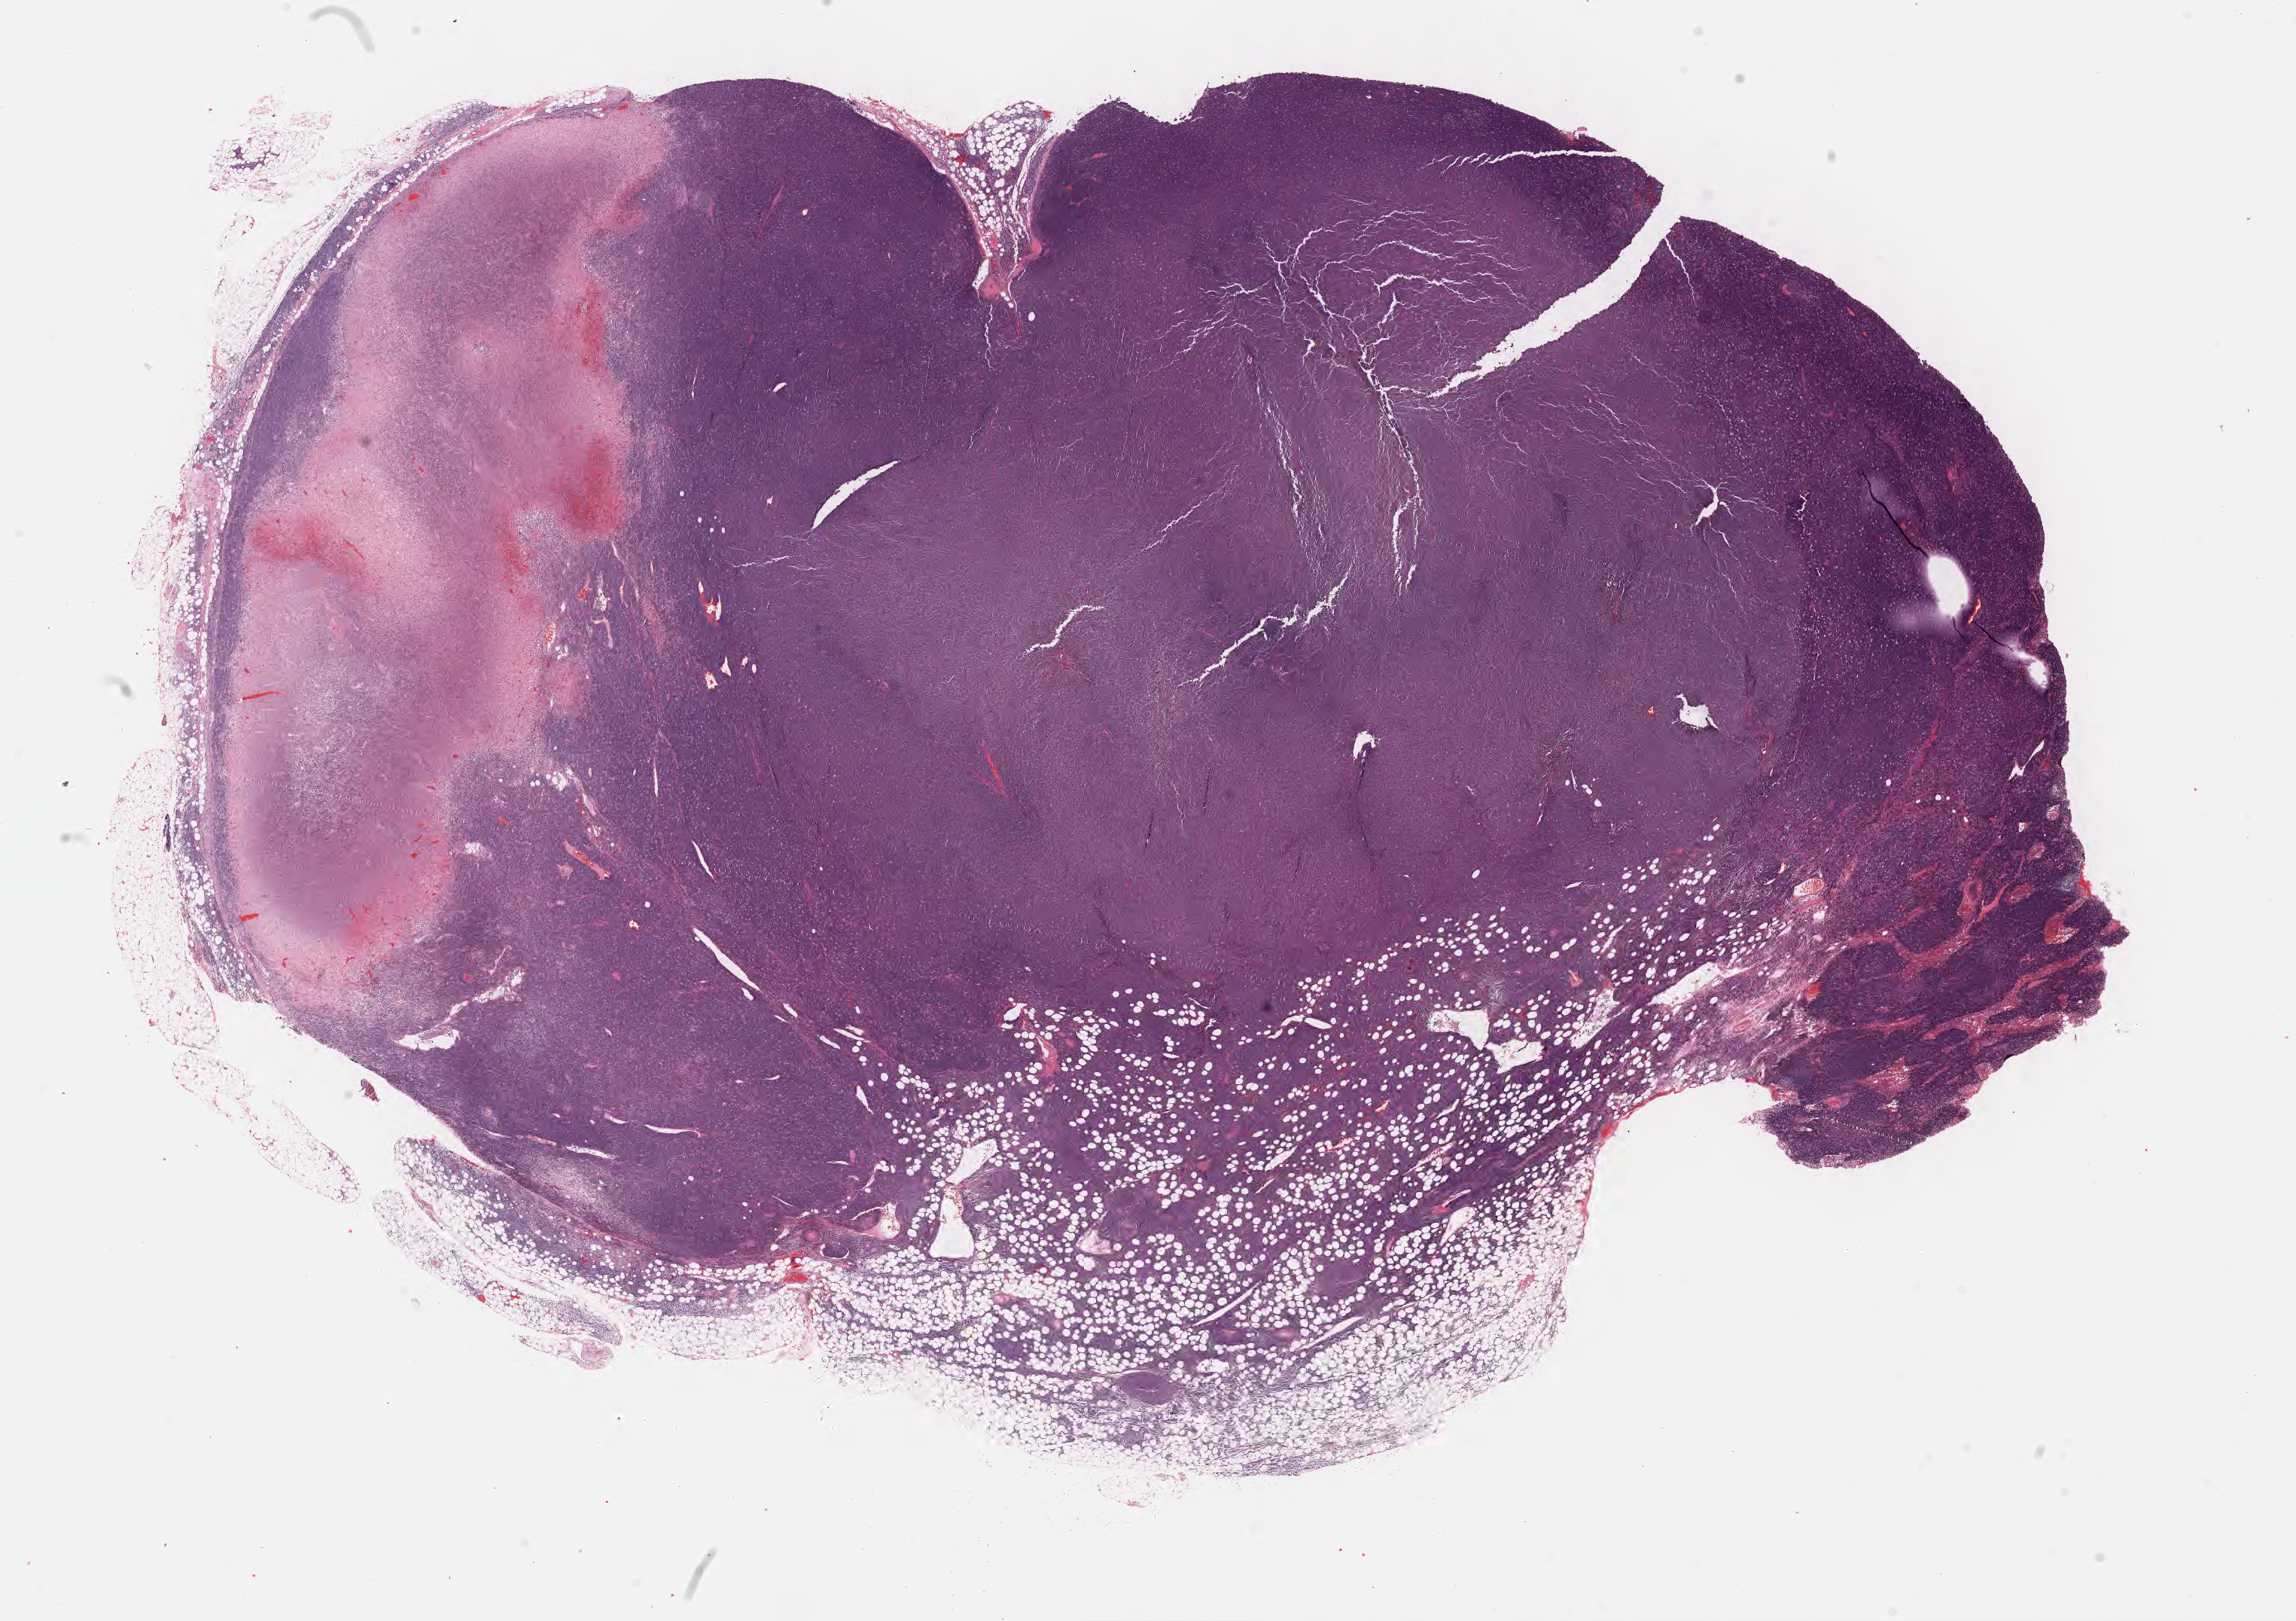
Haematoxylin and eosin whole-slide image — a low-resolution overview of the entire scanned area, about 24.7 x 17.4 mm. FFPE section. Specimen: primary tumor. Male patient, 57 years old. Composition of this section per pathologist review: tumor cells 70%, tumor nuclei 90%, stromal cells 10%, necrosis 20%, normal cells 0%. Inflammatory infiltration, as recorded: lymphocyte infiltration 80%, monocyte infiltration 10%, neutrophil infiltration 5%.
- histologic diagnosis: Burkitt lymphoma, NOS
- Ann Arbor stage (patient): Stage IV